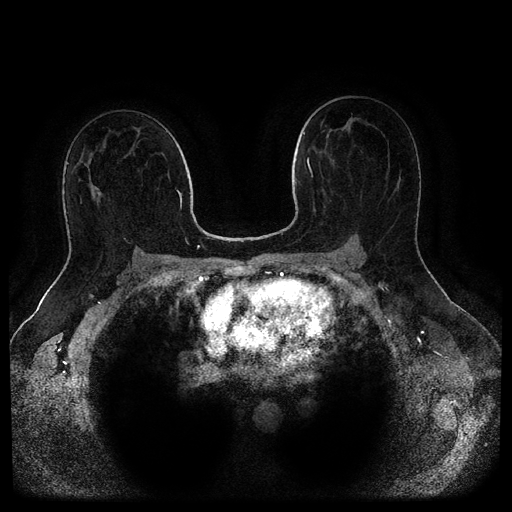
Breast MRI (dynamic contrast-enhanced, multi-phase), one axial slice; dynamic contrast-enhanced series, time point 2 of 5 at this slice position (early post-contrast); 1.5 T; TE 2.6 ms, TR 5.3 ms; 2 mm slice thickness; 512 × 512 image matrix, field of view 370 × 370 mm. Female patient, age 44 years.
Outlined on this slice (semi-automatically segmented with operator editing):
- breast lesion (labelled benign in the annotation): box from (x=92, y=186) to (x=102, y=200) px